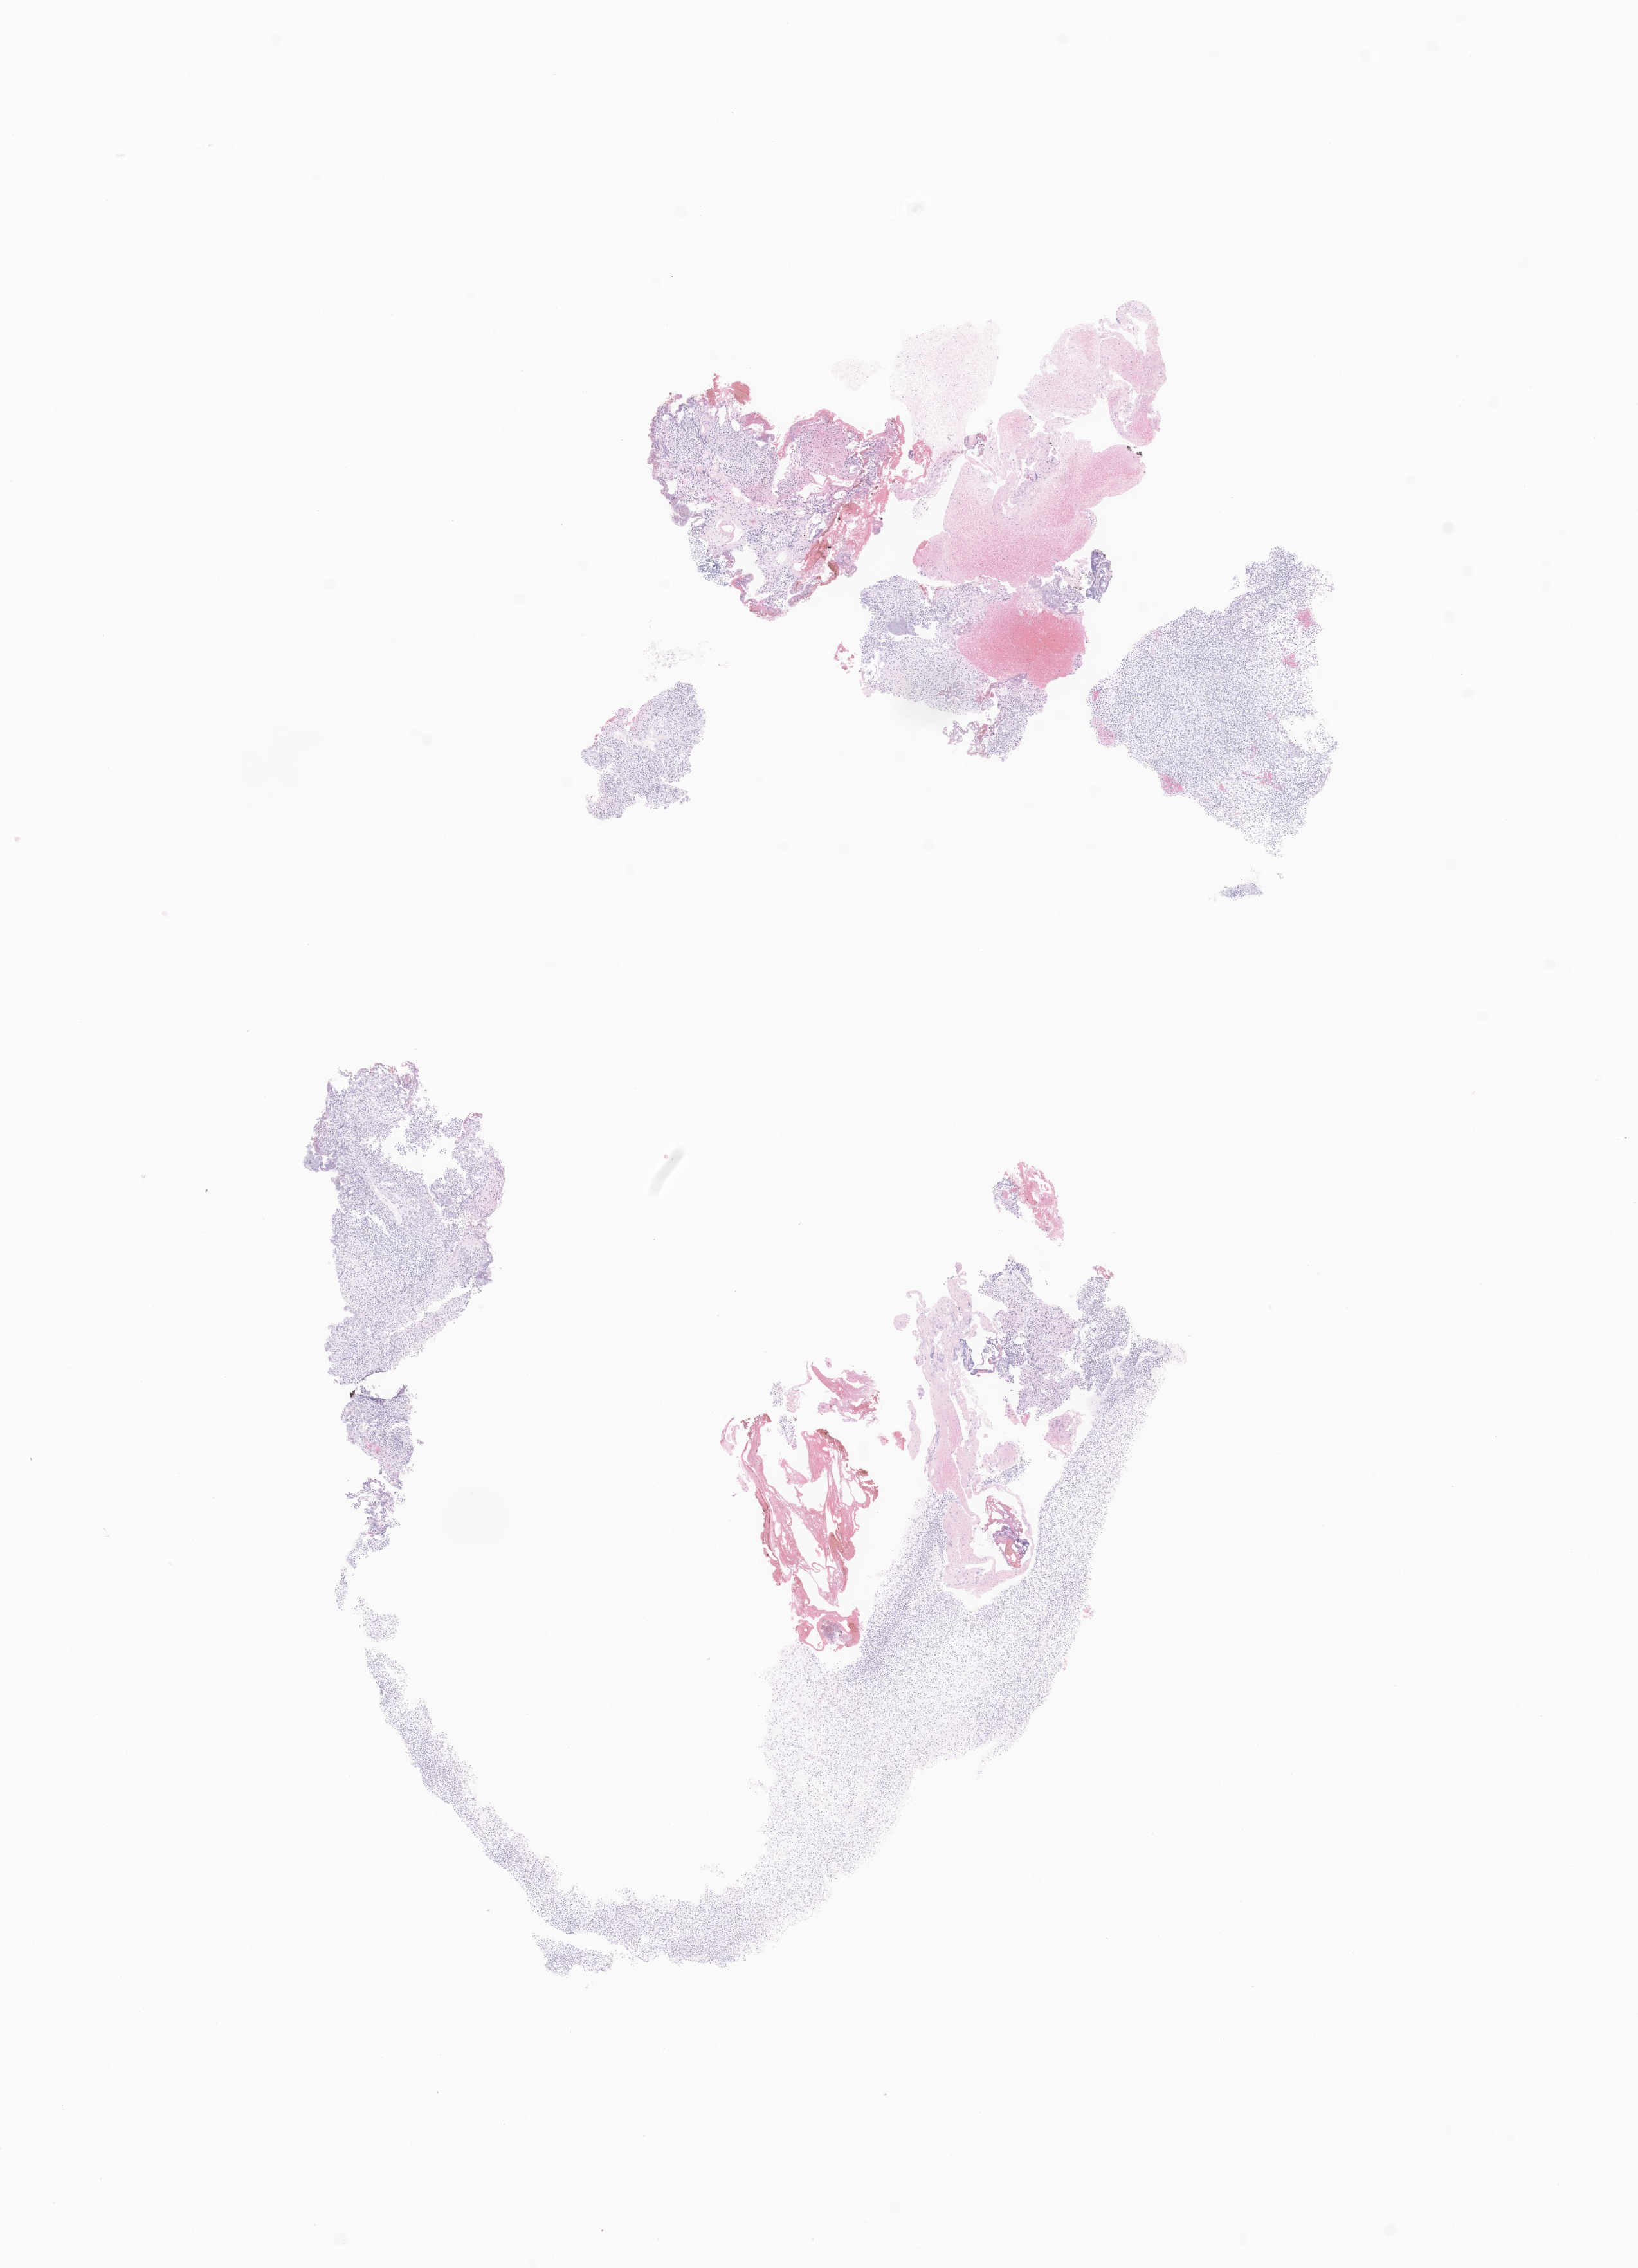
Digitized hematoxylin and eosin (H&E)-stained section of tumor tissue from the urinary bladder, a low-resolution overview of the entire scanned area, about 10.7 x 14.9 mm. Formalin-fixed, paraffin-embedded (FFPE) tissue. Patient male; age 41 months (3 years 5 months).
Diagnosis: Rhabdomyosarcoma, NOS.